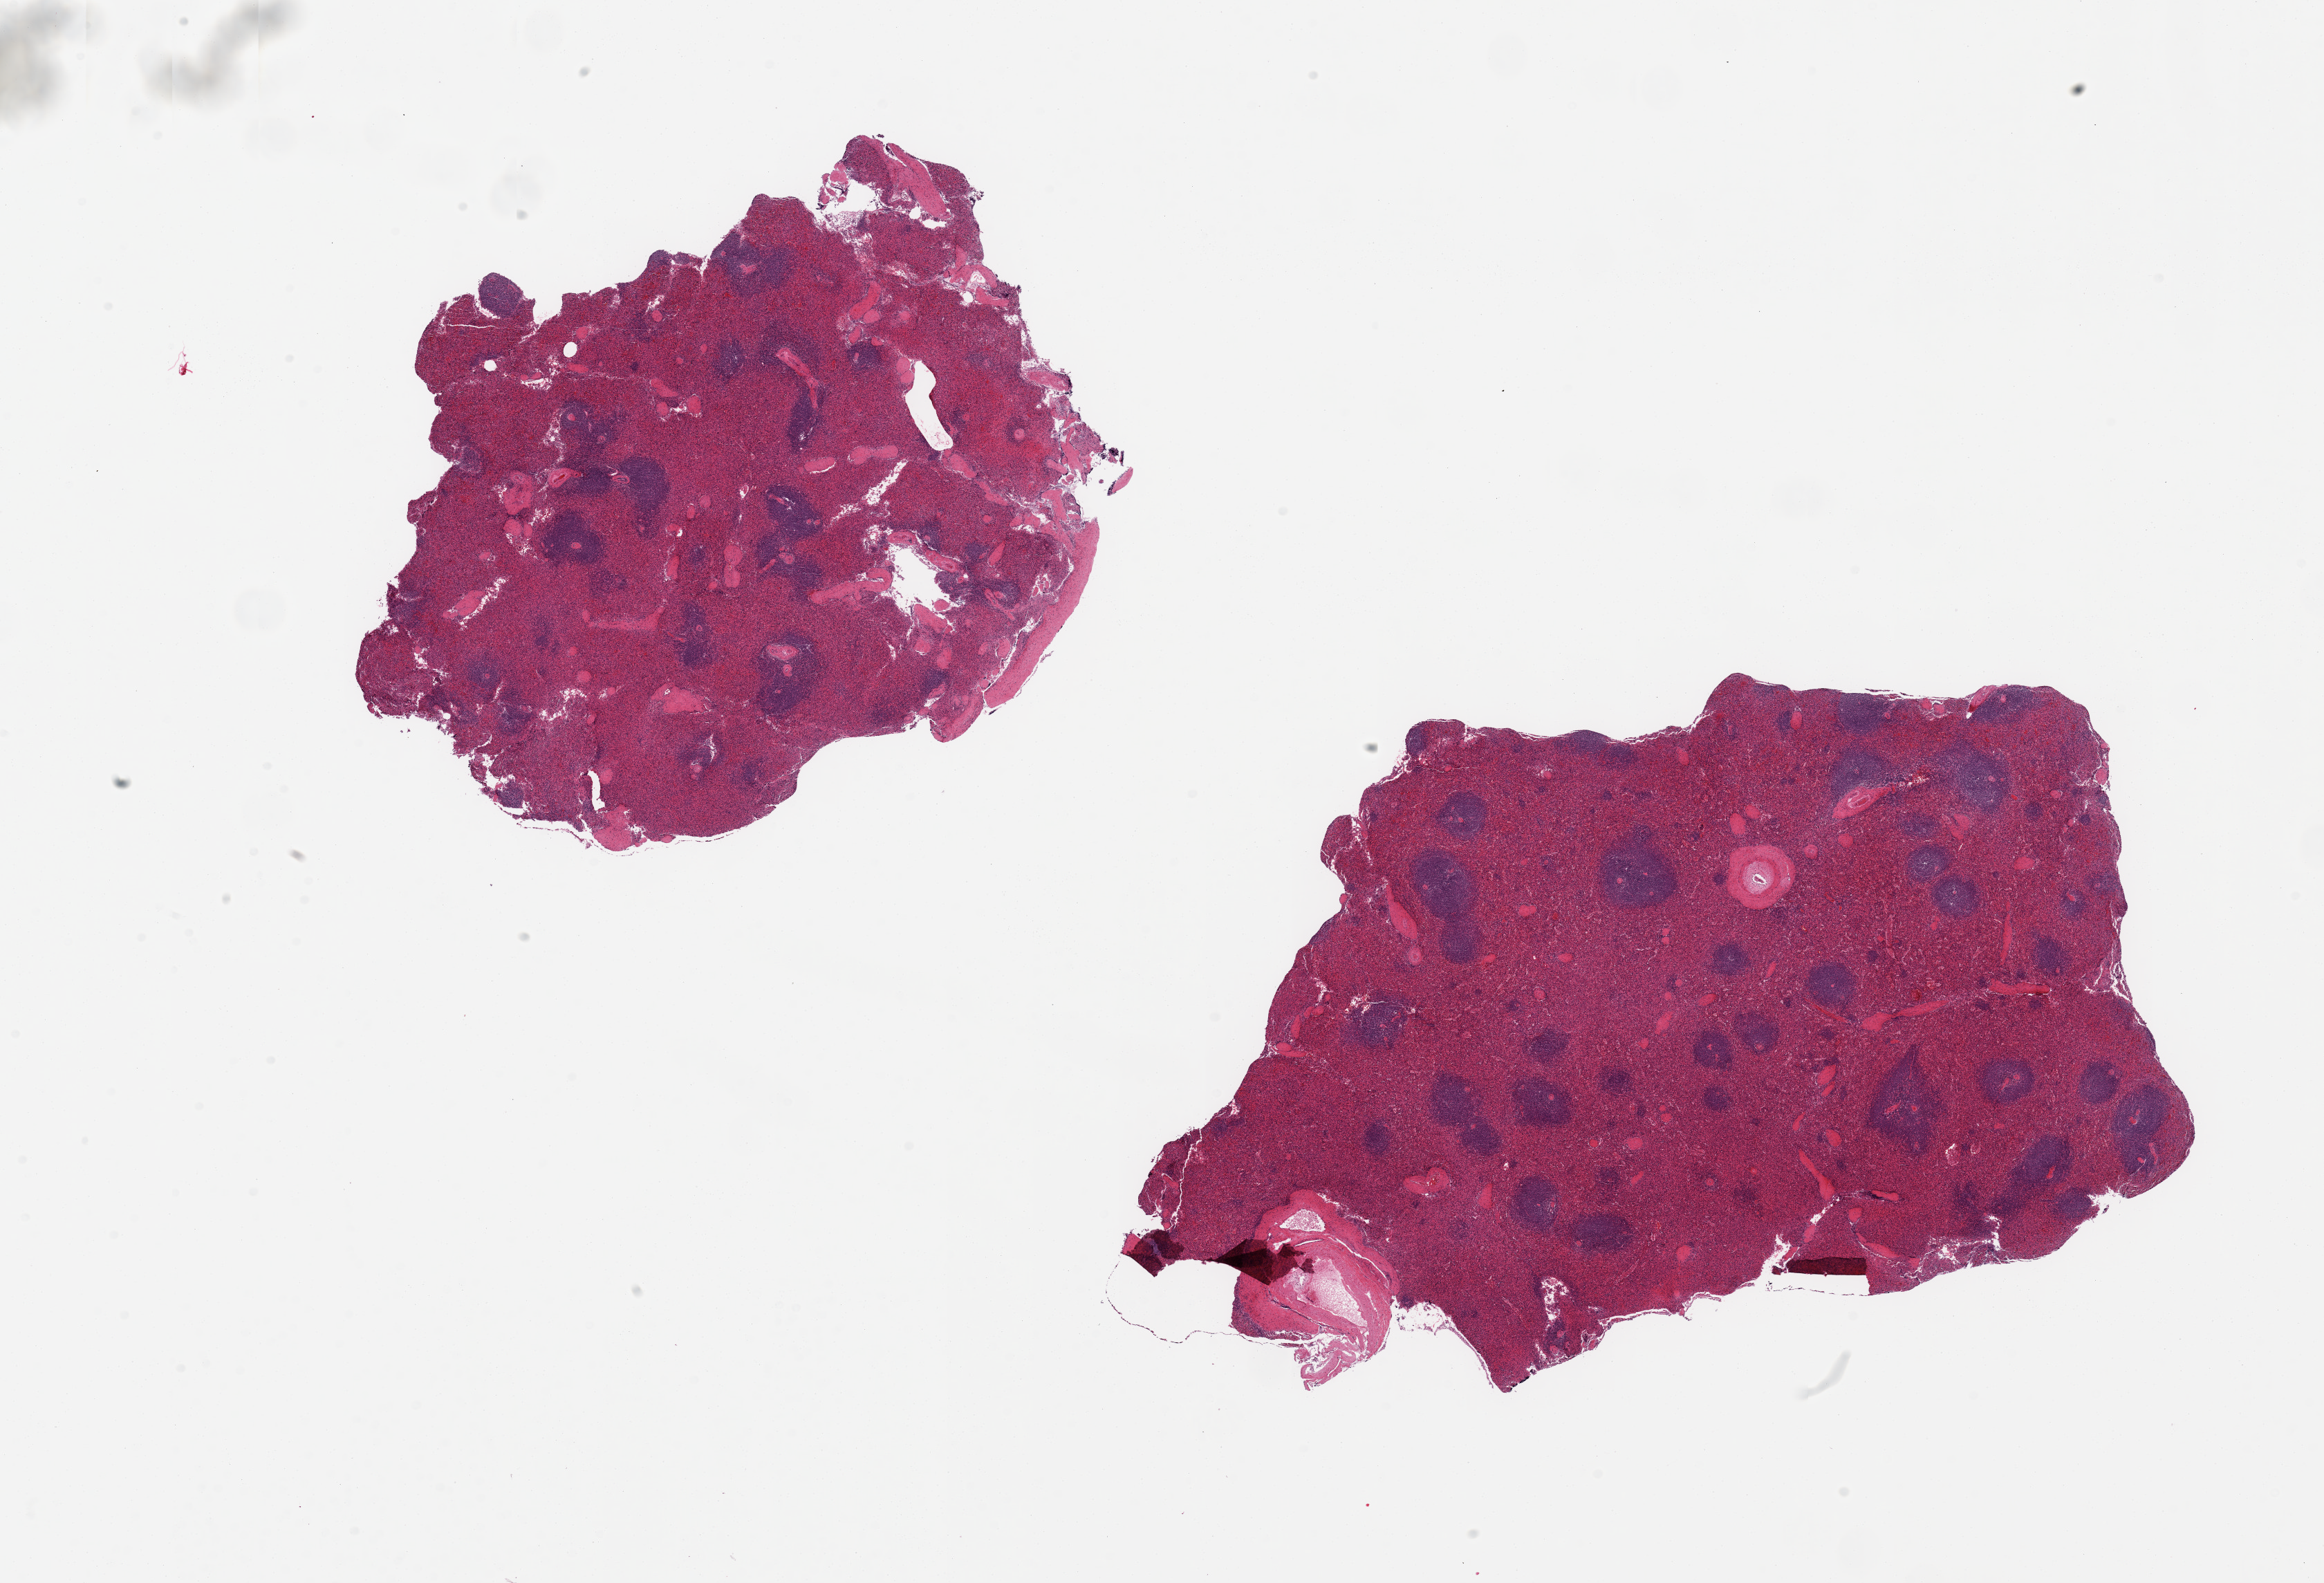
Whole-slide image, hematoxylin and eosin (H&E) stain, brightfield, shown as a low-resolution overview of the whole scanned area (about 26.6 x 18.1 mm), PAXgene-fixed, paraffin-embedded tissue, section of spleen (target tissue), donor tissue sample. Donor sex: male.
Review note (as recorded): 2 pieces; congestion; small fragment of capsule; larger vessel included.